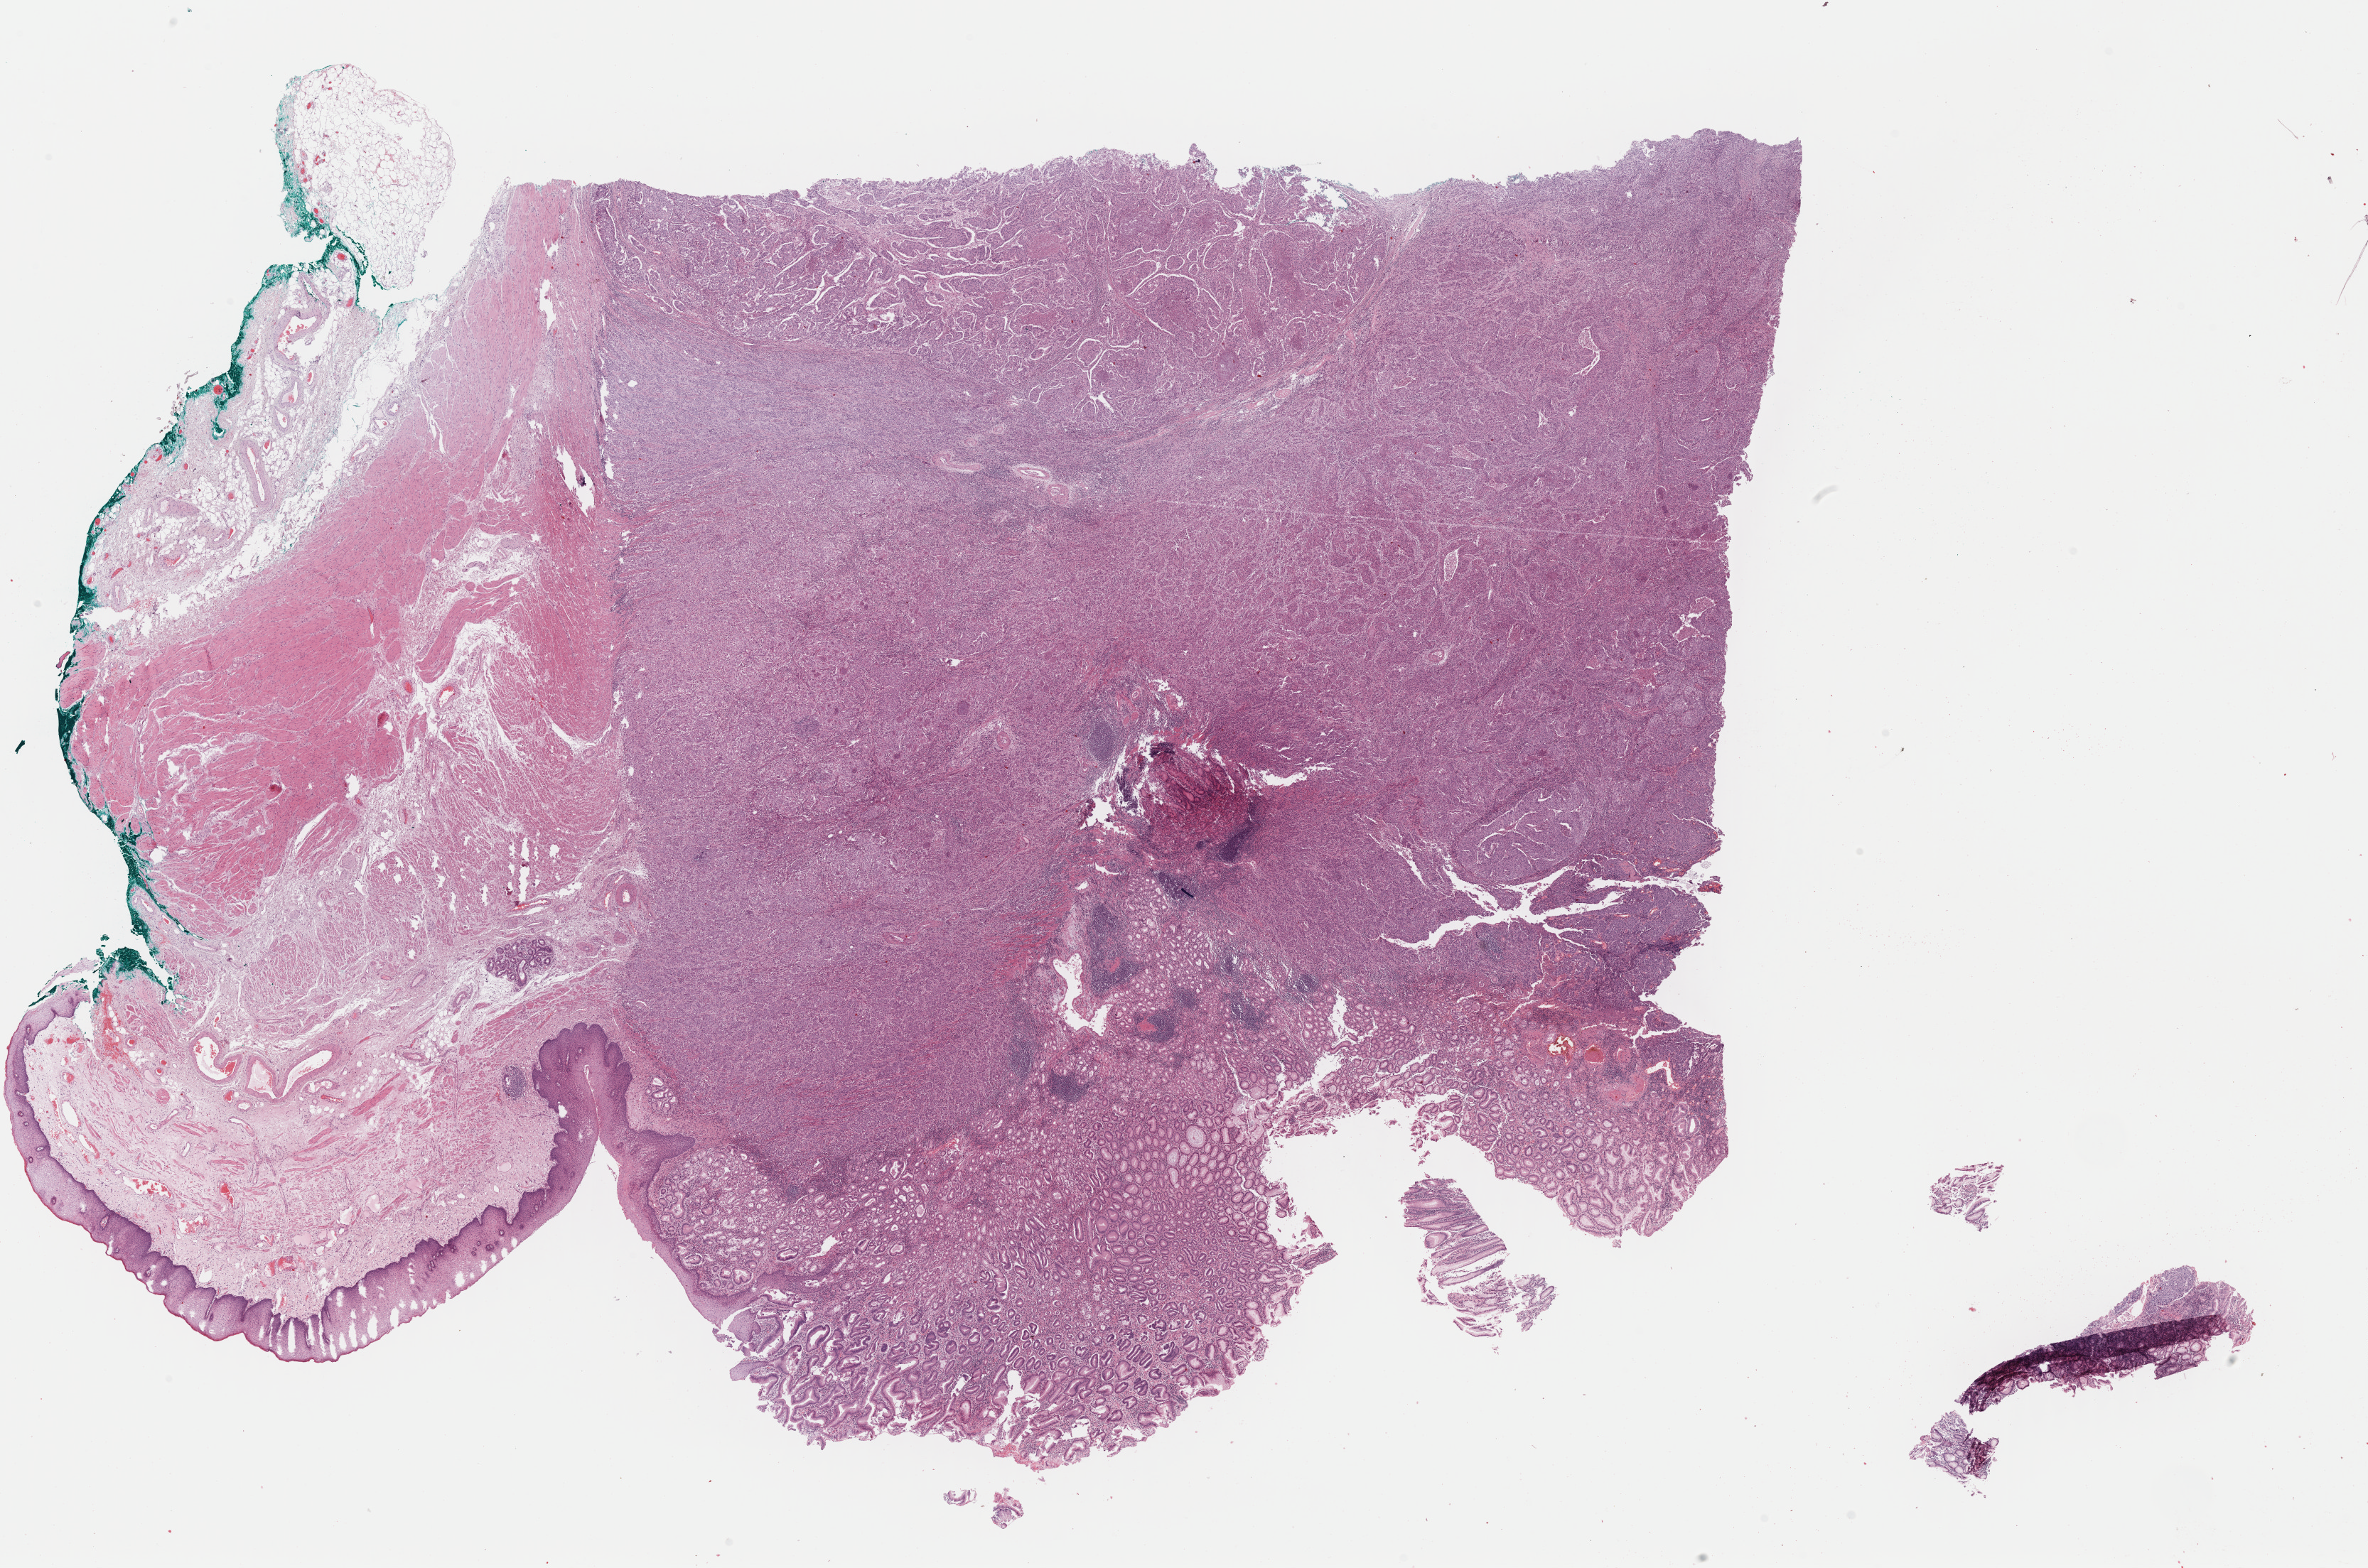
Whole-slide histology image, Hematoxylin and eosin (H&E) stained, low-resolution overview of the scanned area, about 26.3 x 17.4 mm, FFPE section, sample: primary tumour, stomach. Male patient; age at initial diagnosis 63 years. Histologic grade: G3 (poorly differentiated).
Lymph nodes positive (case pathology): 1 of 19 examined. Histologic diagnosis: Adenocarcinoma, NOS (fundus of stomach). AJCC pathologic stage: IIB.